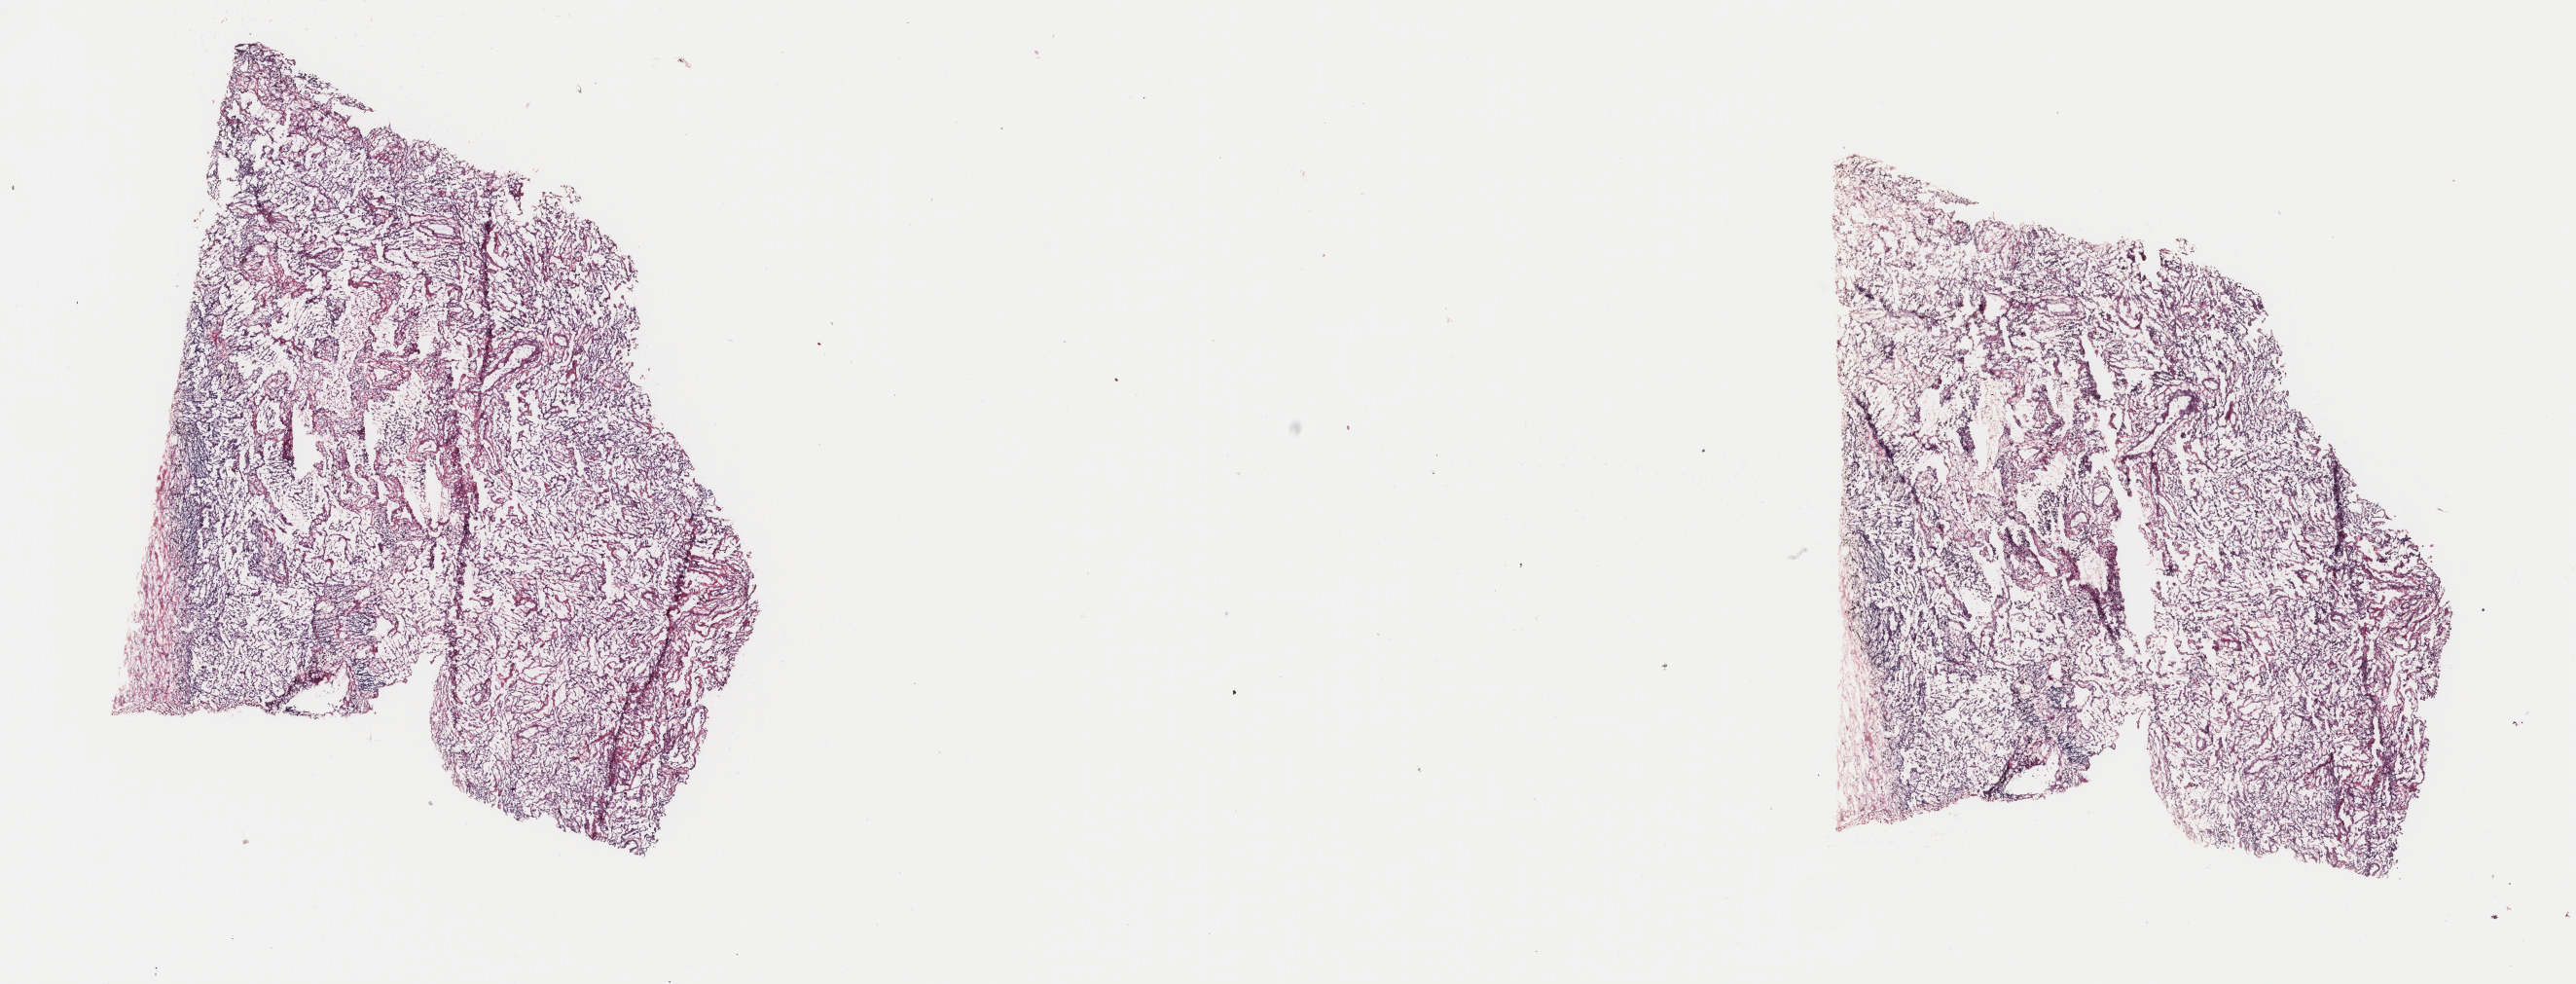
Digitized H&E tissue section (whole slide), shown as a low-resolution overview of the whole scanned area (about 21.0 x 8.0 mm, slide scanned at 40x). Frozen section from the top of the tissue portion. Sample: primary tumour, mesothelium. Male patient; age at initial diagnosis 69 years. Slide review estimates, as recorded: tumour cells 100%, tumour nuclei 85%, normal cells 0%, stromal cells 0%, necrosis 0%. Infiltration values recorded for this section: lymphocyte infiltration 0%, monocyte infiltration 0%, neutrophil infiltration 0%.
* laterality: left
* AJCC pathologic stage: III
* diagnosis: Epithelioid mesothelioma, malignant (pleura, NOS)
* TNM: T2 N1 M0